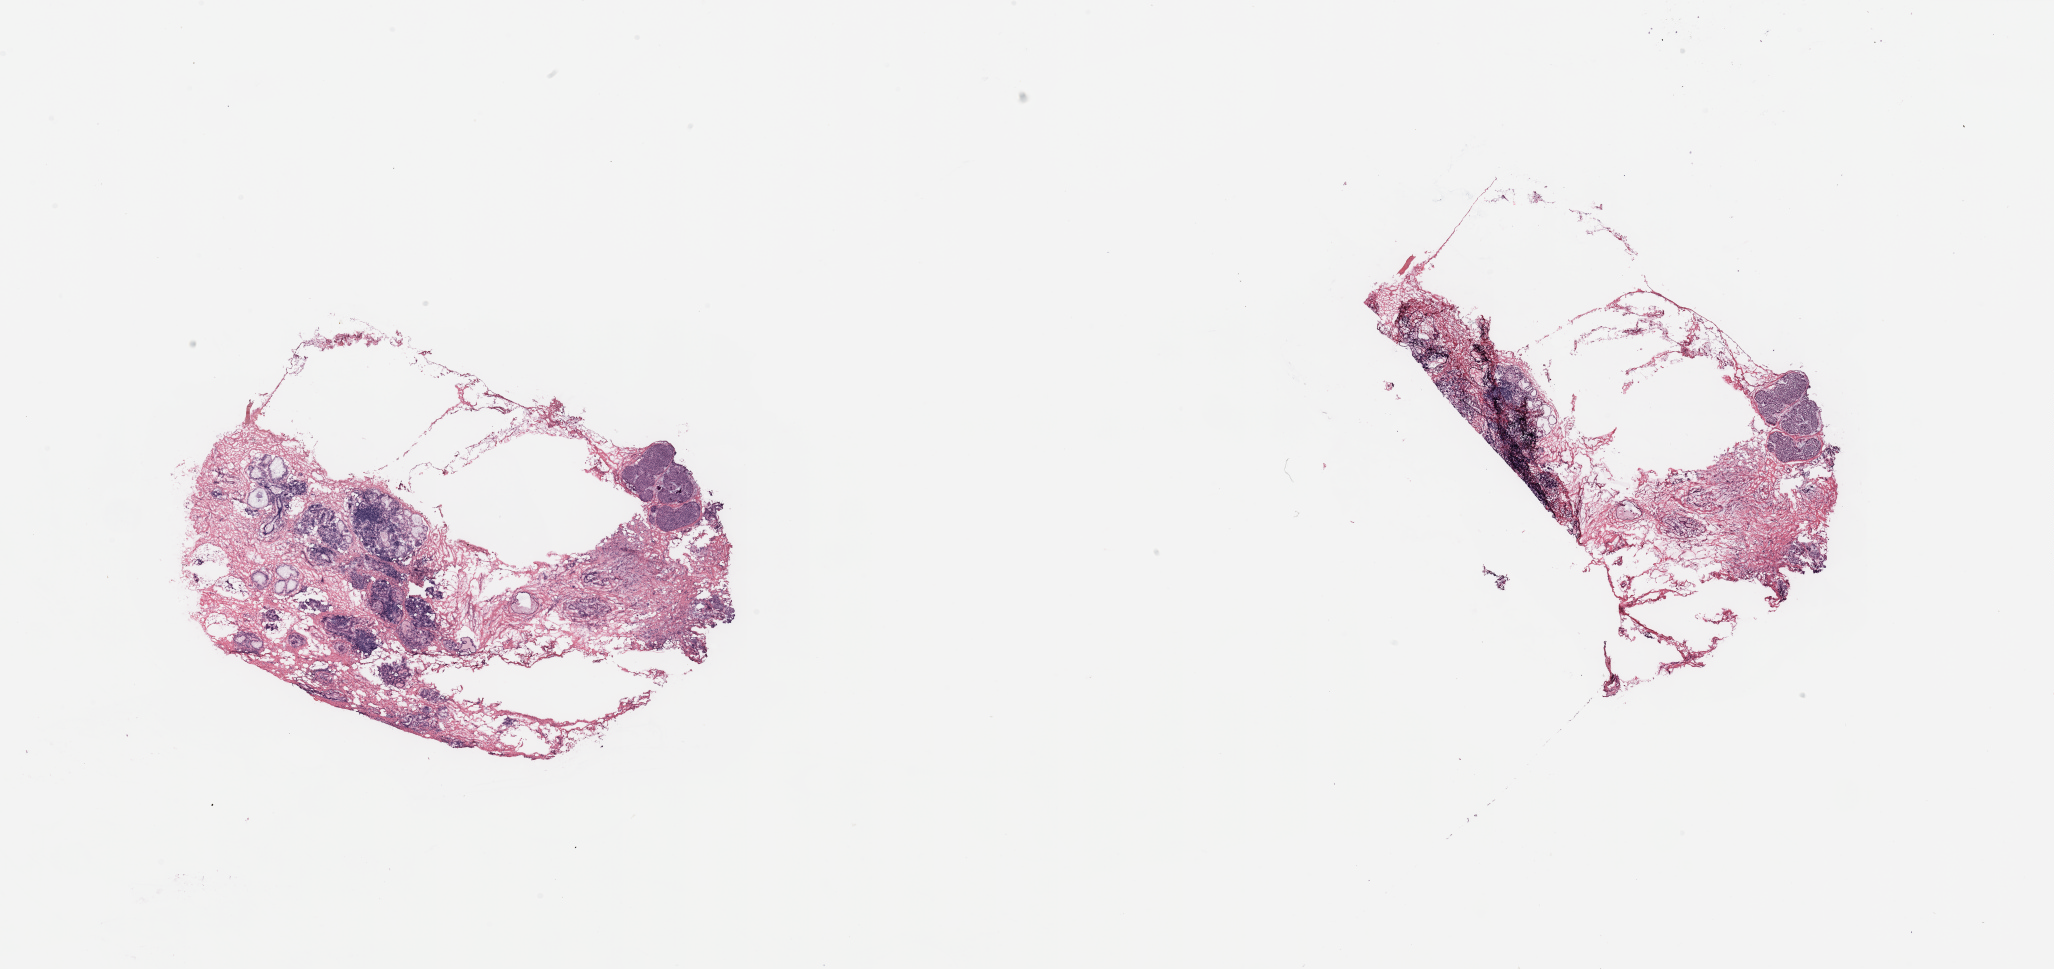
H&E whole-slide image — low-resolution overview of the scanned area, about 32.5 x 15.3 mm. Breast, tissue type not recorded.
• patient diagnosis (cohort enrolment): breast cancer (breast)